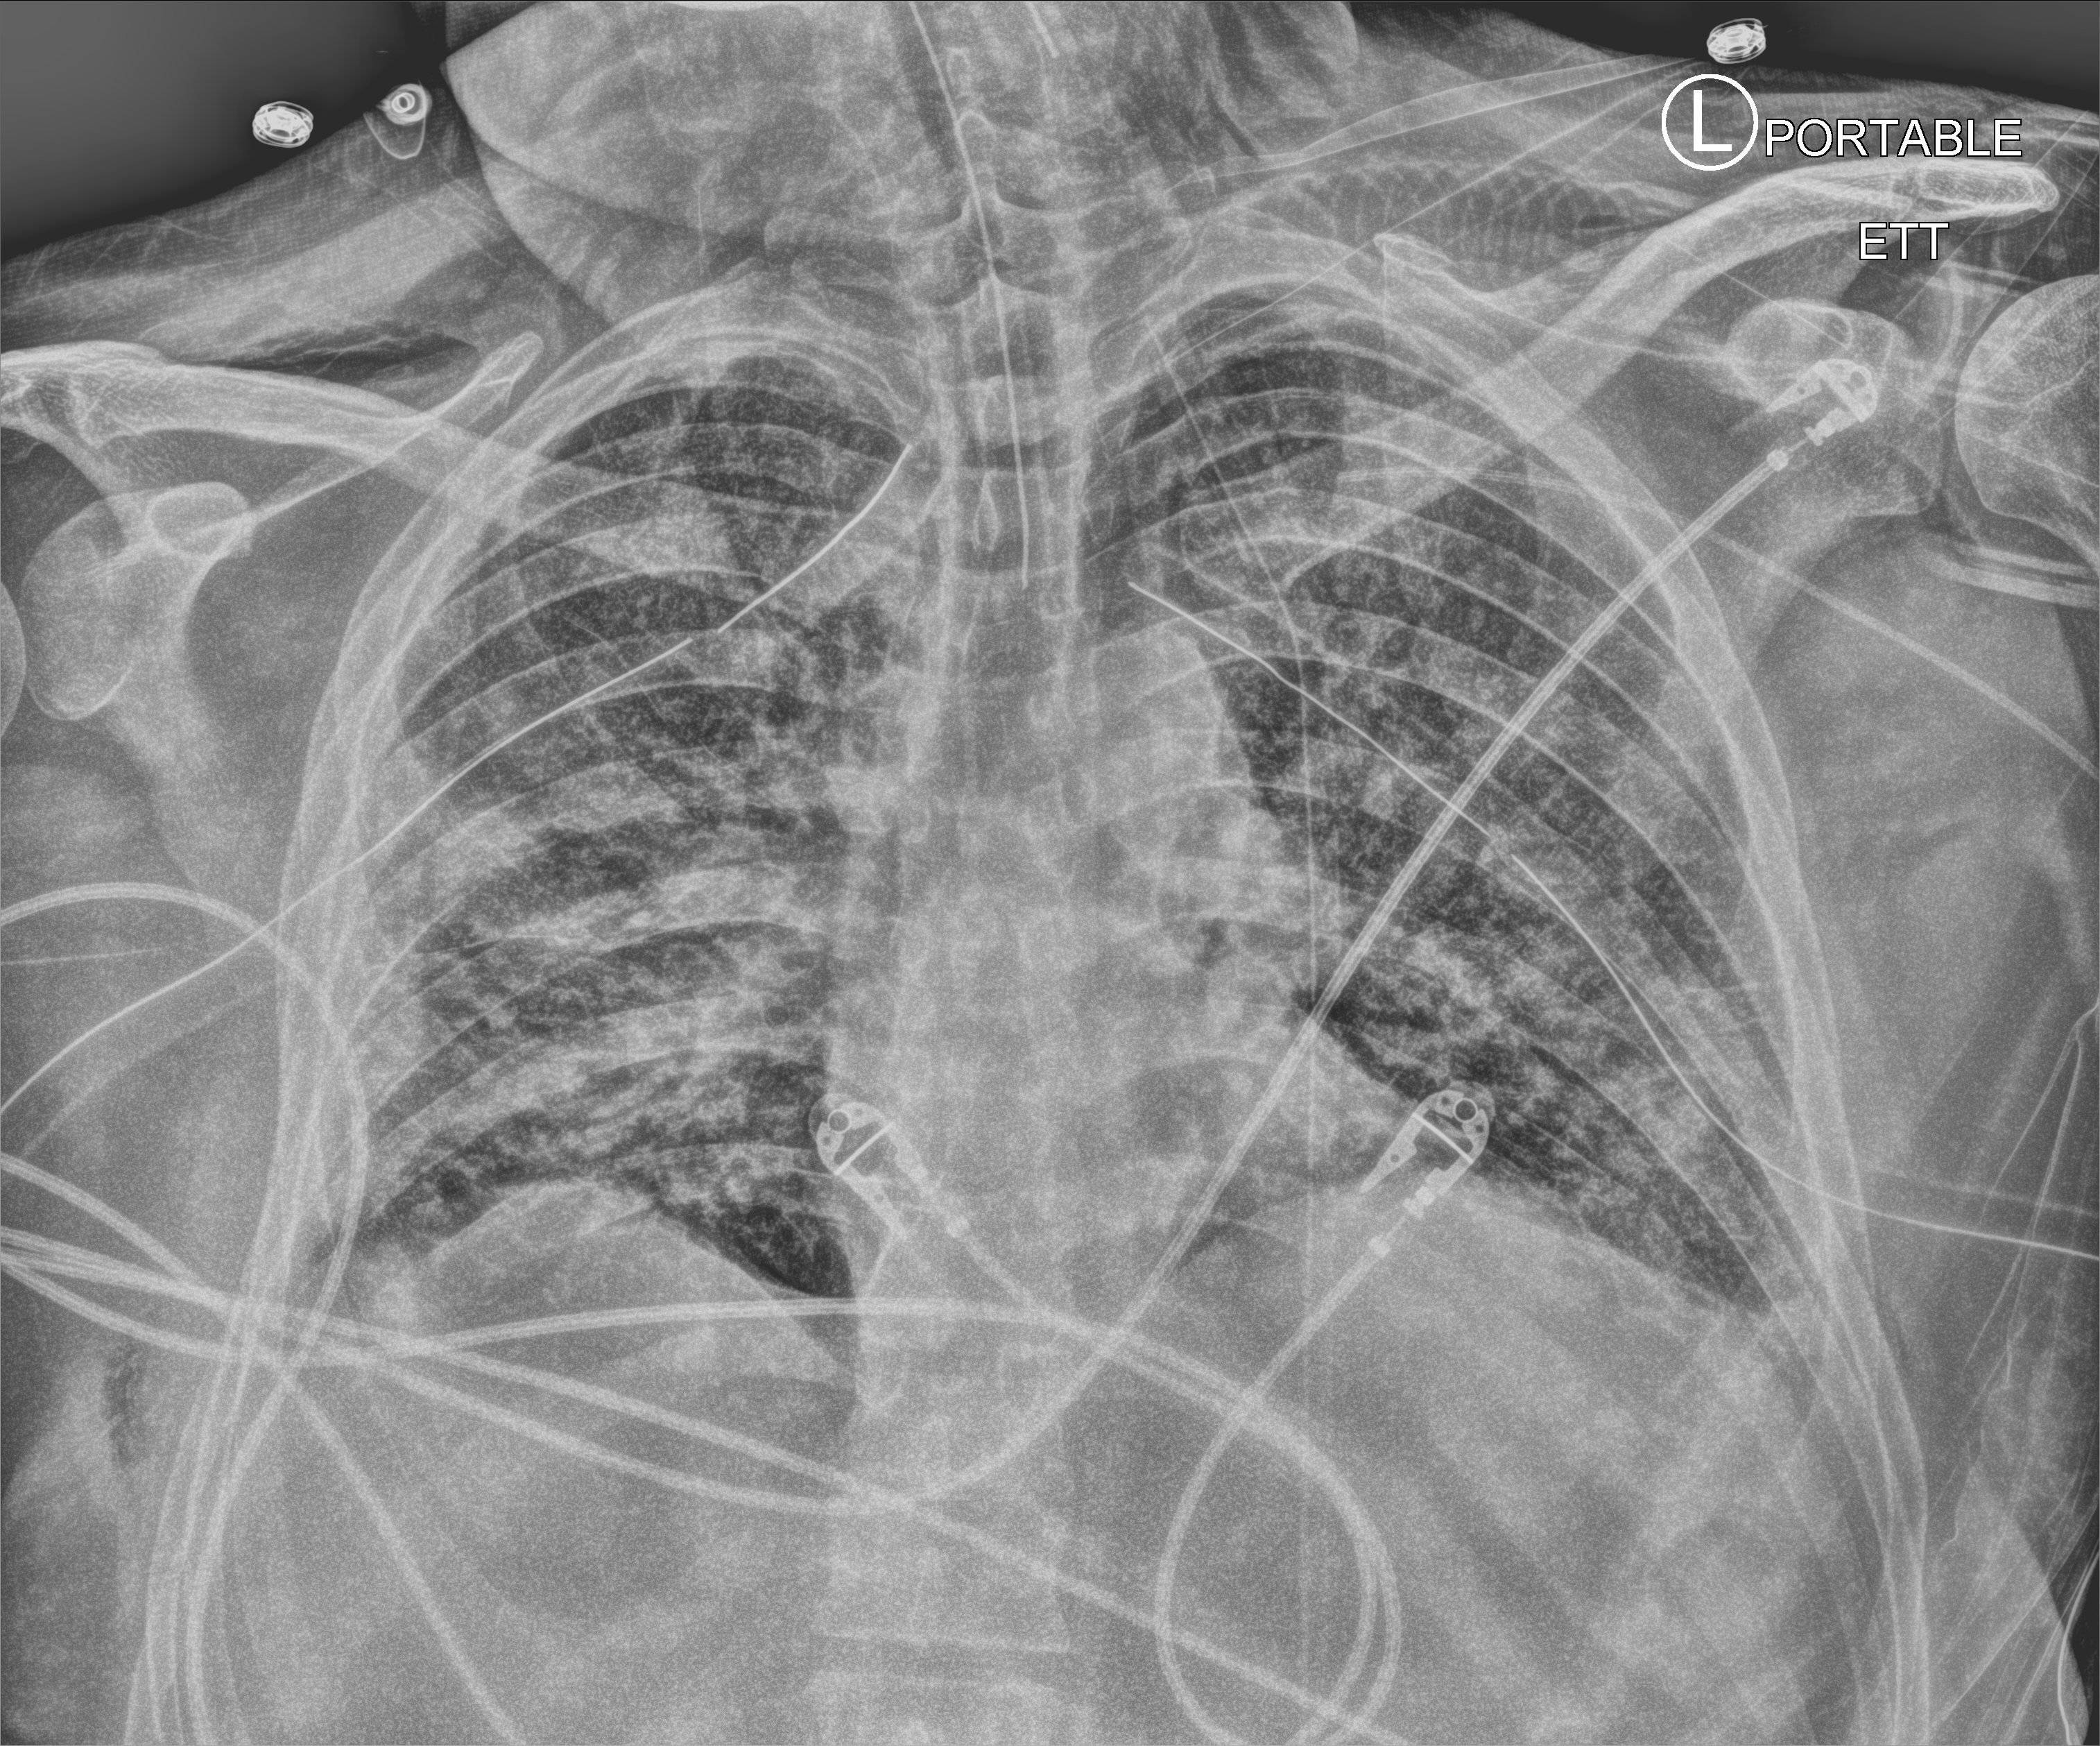
Chest X-ray (portable), anteroposterior (AP) projection. Patient hospitalised with COVID-19; male, aged 18–59 years.
Admission-level facts for this patient (not findings on this image; timing relative to this image not recorded): chronic kidney disease (admission record): no.